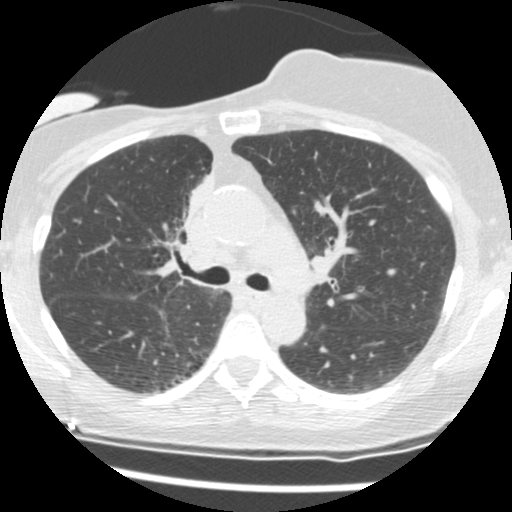
Chest CT (low-dose screening protocol), one axial image, second annual screen, lung window (W 1500 / L -600 HU), 2.5 mm slice thickness, standard (soft-tissue) reconstruction kernel (STANDARD), slice 49 of 165 in the series. Female, age 56 years at enrolment. Current smoker at enrolment.
Expert reader's lesion annotation, box from (x=153, y=174) to (x=209, y=263) px. The screening reader recorded 2 non-calcified nodules or masses ≥4 mm on this exam (right middle lobe, right lower lobe); which of them this box marks is not recorded. Later outcome: lung cancer diagnosed 675 days after this screen (after the third annual screen) — adenocarcinoma, NOS, right upper lobe, stage IIIB (AJCC 6th edition), 8 mm at pathology.